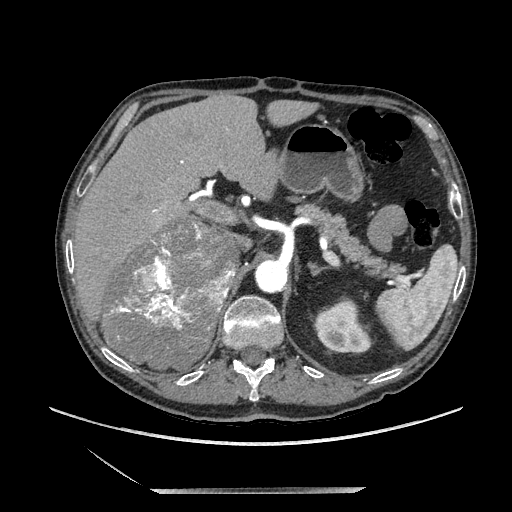
Contrast-enhanced abdominal CT, one axial slice; position 139 of 243 along the scan axis; soft-tissue window (W 400 / L 40 HU); 512 × 512 image matrix, field of view 420 × 420 mm. Male patient. Case-level facts recorded for this patient, not image findings: diagnosis: adrenocortical carcinoma; tumour side: right adrenal; tumour size at pathology: 16 cm; Ki-67 index: 17 %; stage (as recorded): 3.
Outlined on this slice (semi-automatically segmented with operator editing):
- mass: box from (x=106, y=221) to (x=236, y=368) px